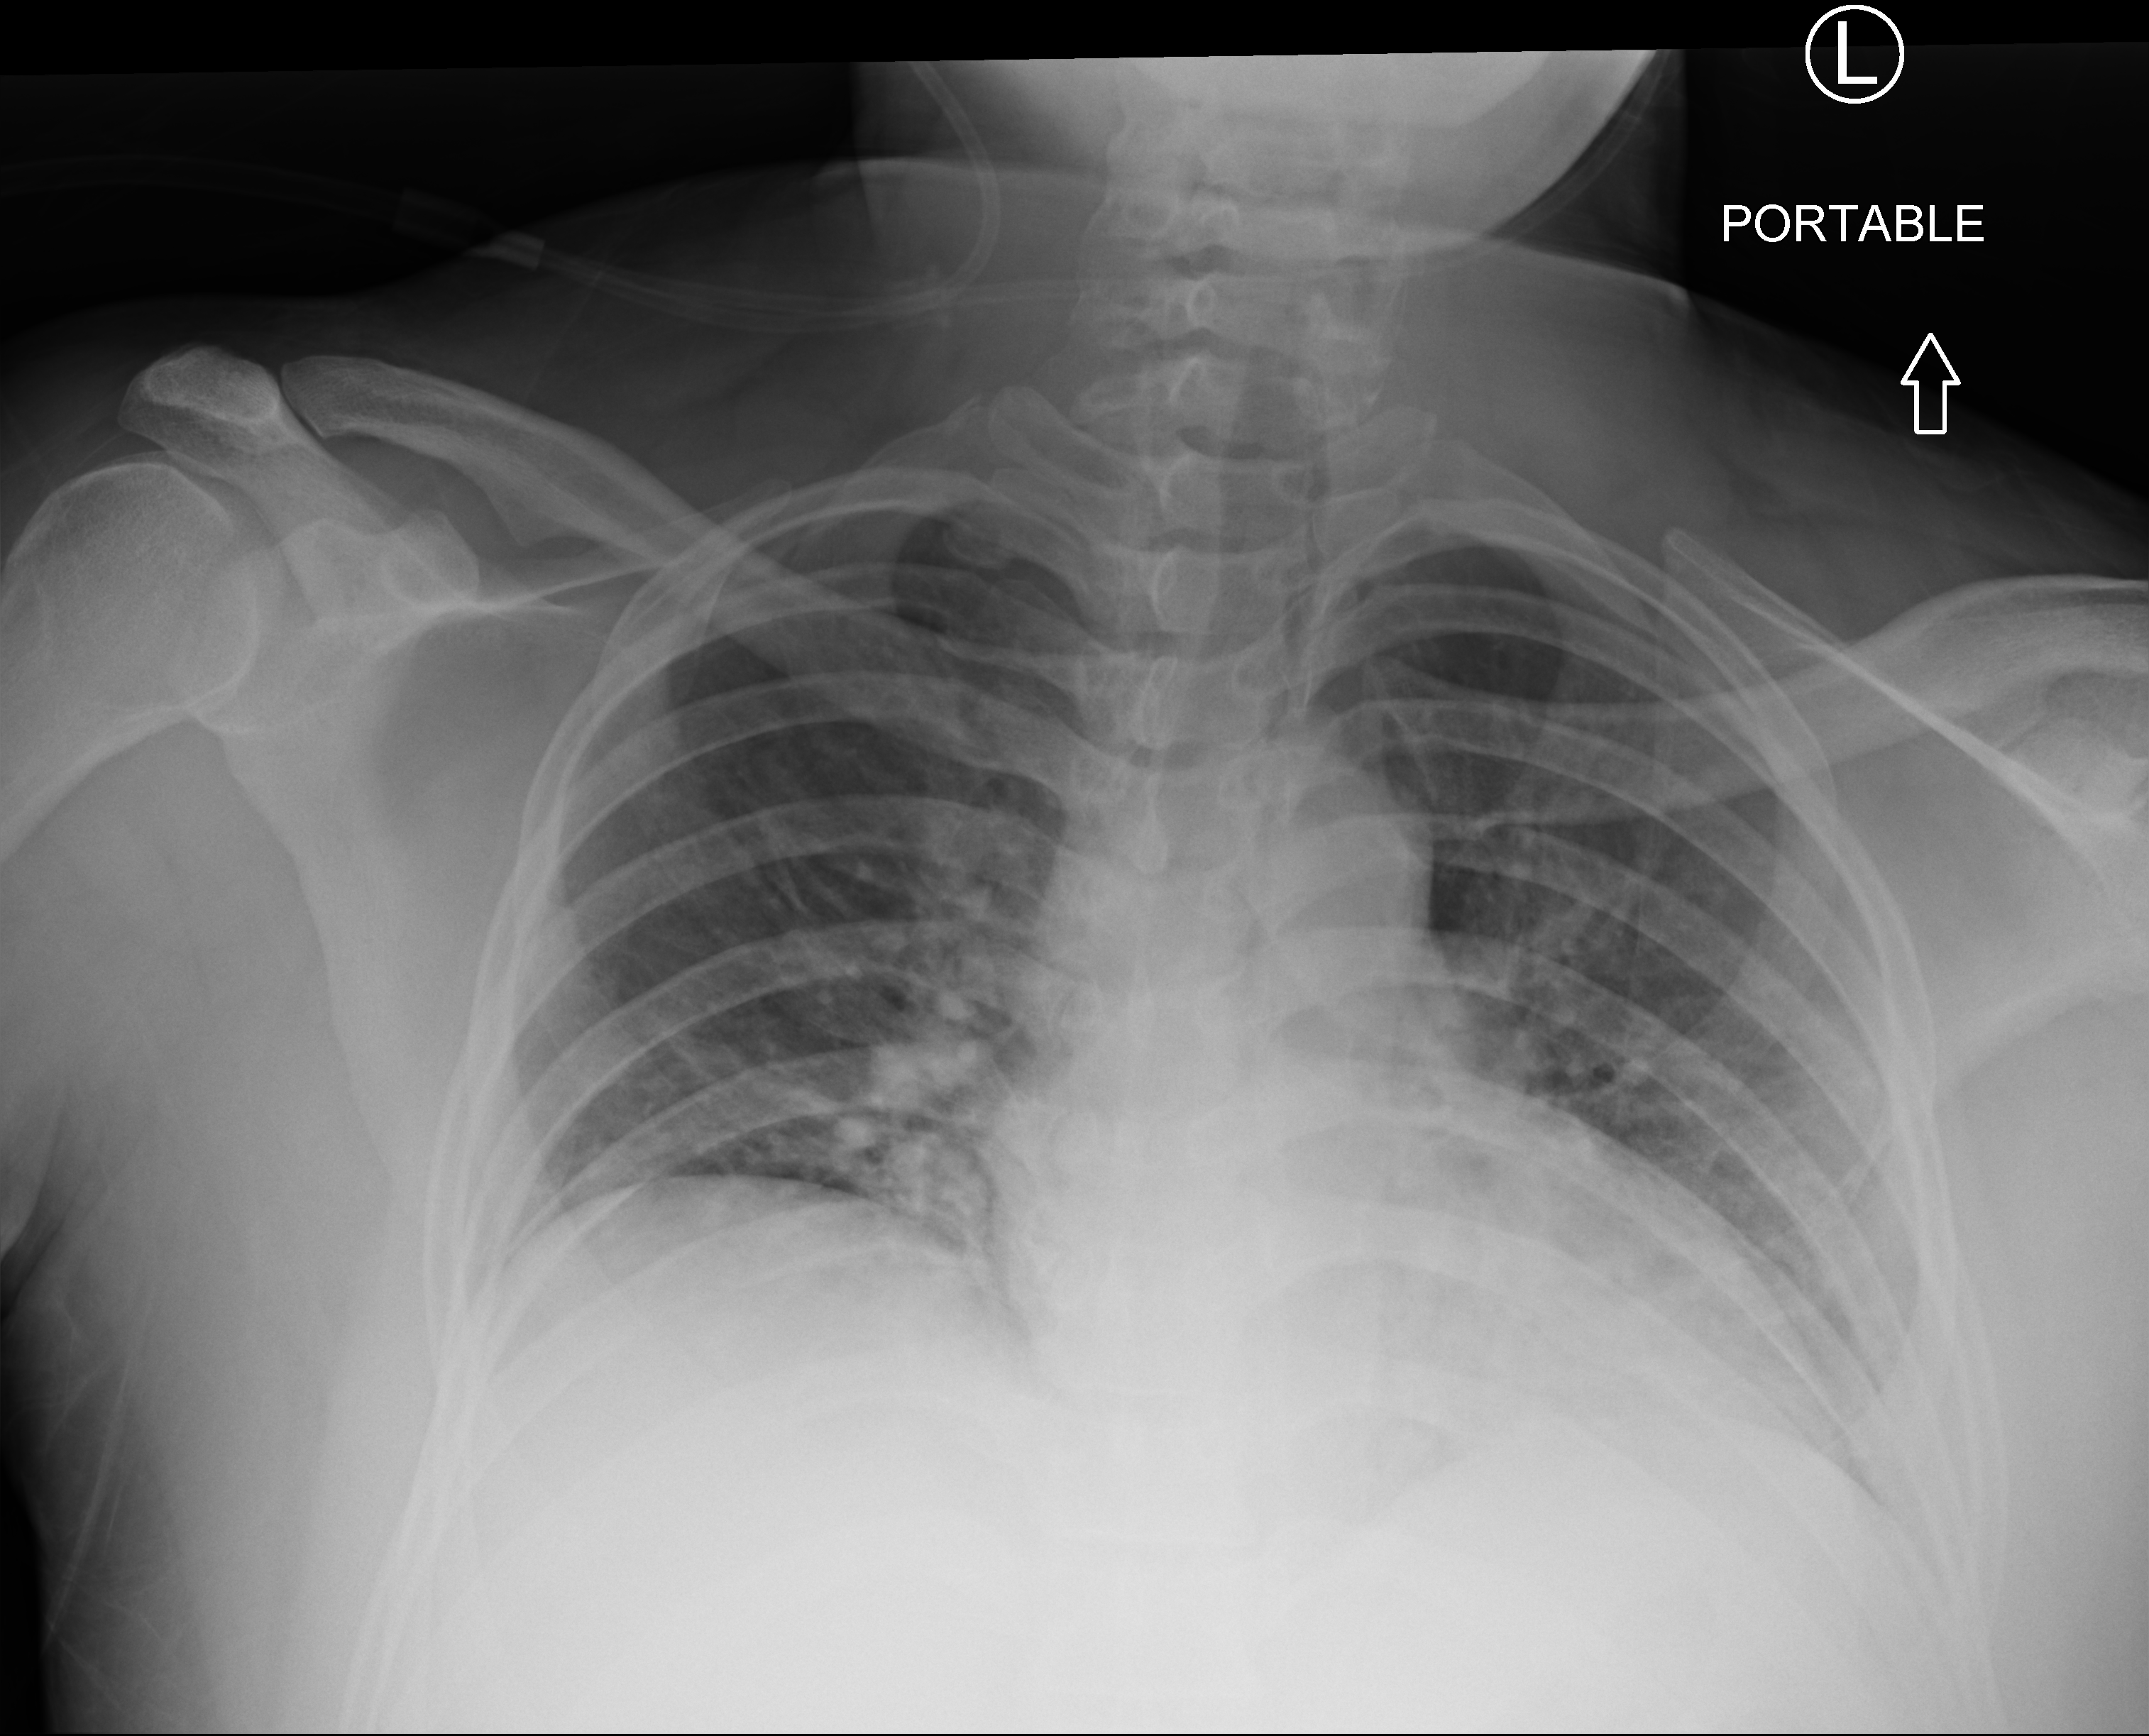
Portable chest radiograph; anteroposterior (AP) projection. Patient hospitalised with COVID-19; male, aged 18–59 years.
Admission-level facts for this patient (not findings on this image; timing relative to this image not recorded): admitted to intensive care during this hospital stay: no; mechanically ventilated during this hospital stay: no.